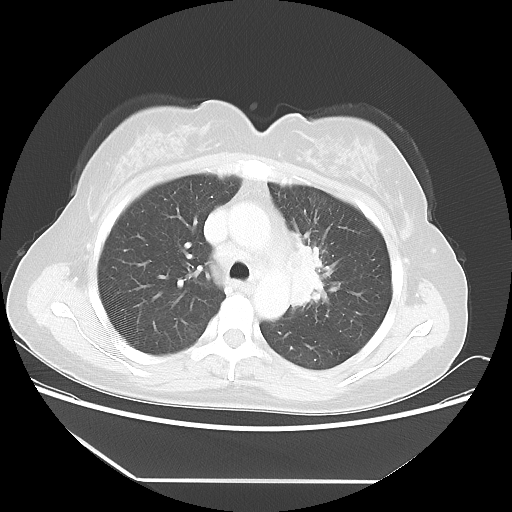
Chest CT, one axial slice. Position 36 of 52 along the scan axis. Reconstruction kernel LUNG. 100 kVp. Lung window (W 1500 / L -600 HU). 512 × 512 image matrix, field of view 390 × 390 mm. Patient: female, 50 years. From the clinical record (not read from this slice): clinical TNM (as recorded): T2 N3 M0.
Annotated regions visible in this slice (rectangle marked by the reading radiologist):
- lung tumour (recorded histology: adenocarcinoma): box from (x=278, y=226) to (x=344, y=318) px